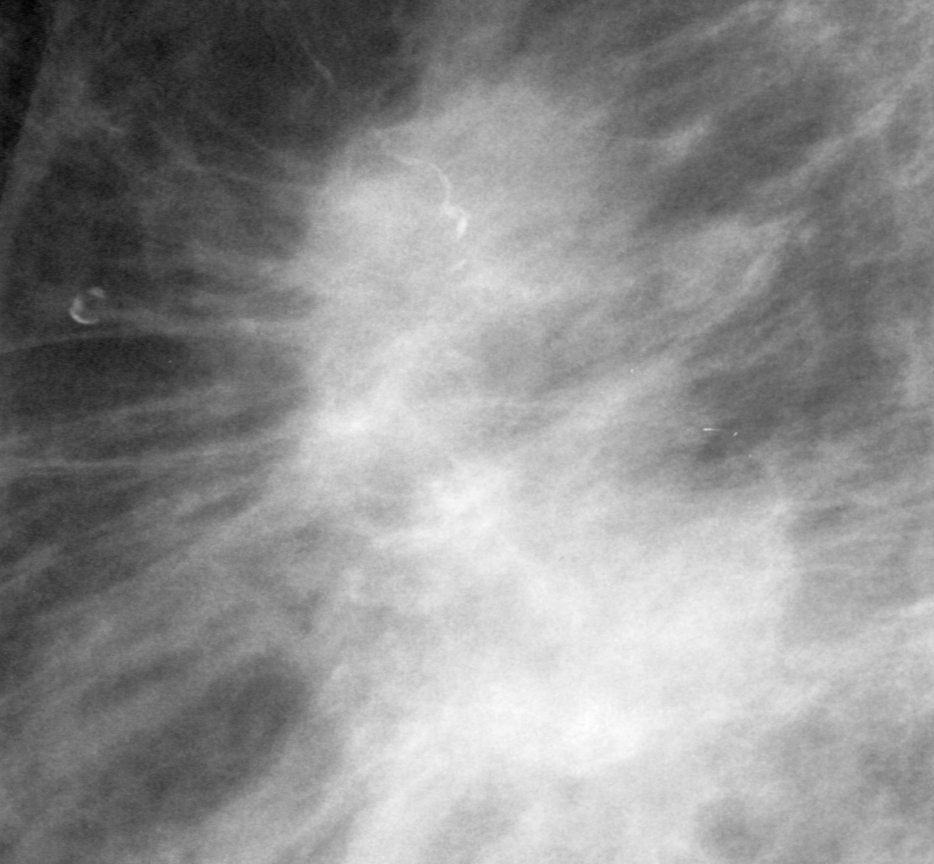
Cropped region of a digitized screen-film mammogram centred on a radiologist-marked abnormality; left breast; MLO view.
Finding: mass, shape irregular, margins spiculated; BI-RADS assessment category 5; subtlety rating 5 on a 1 (subtle) to 5 (obvious) scale; pathology (as recorded): malignant.